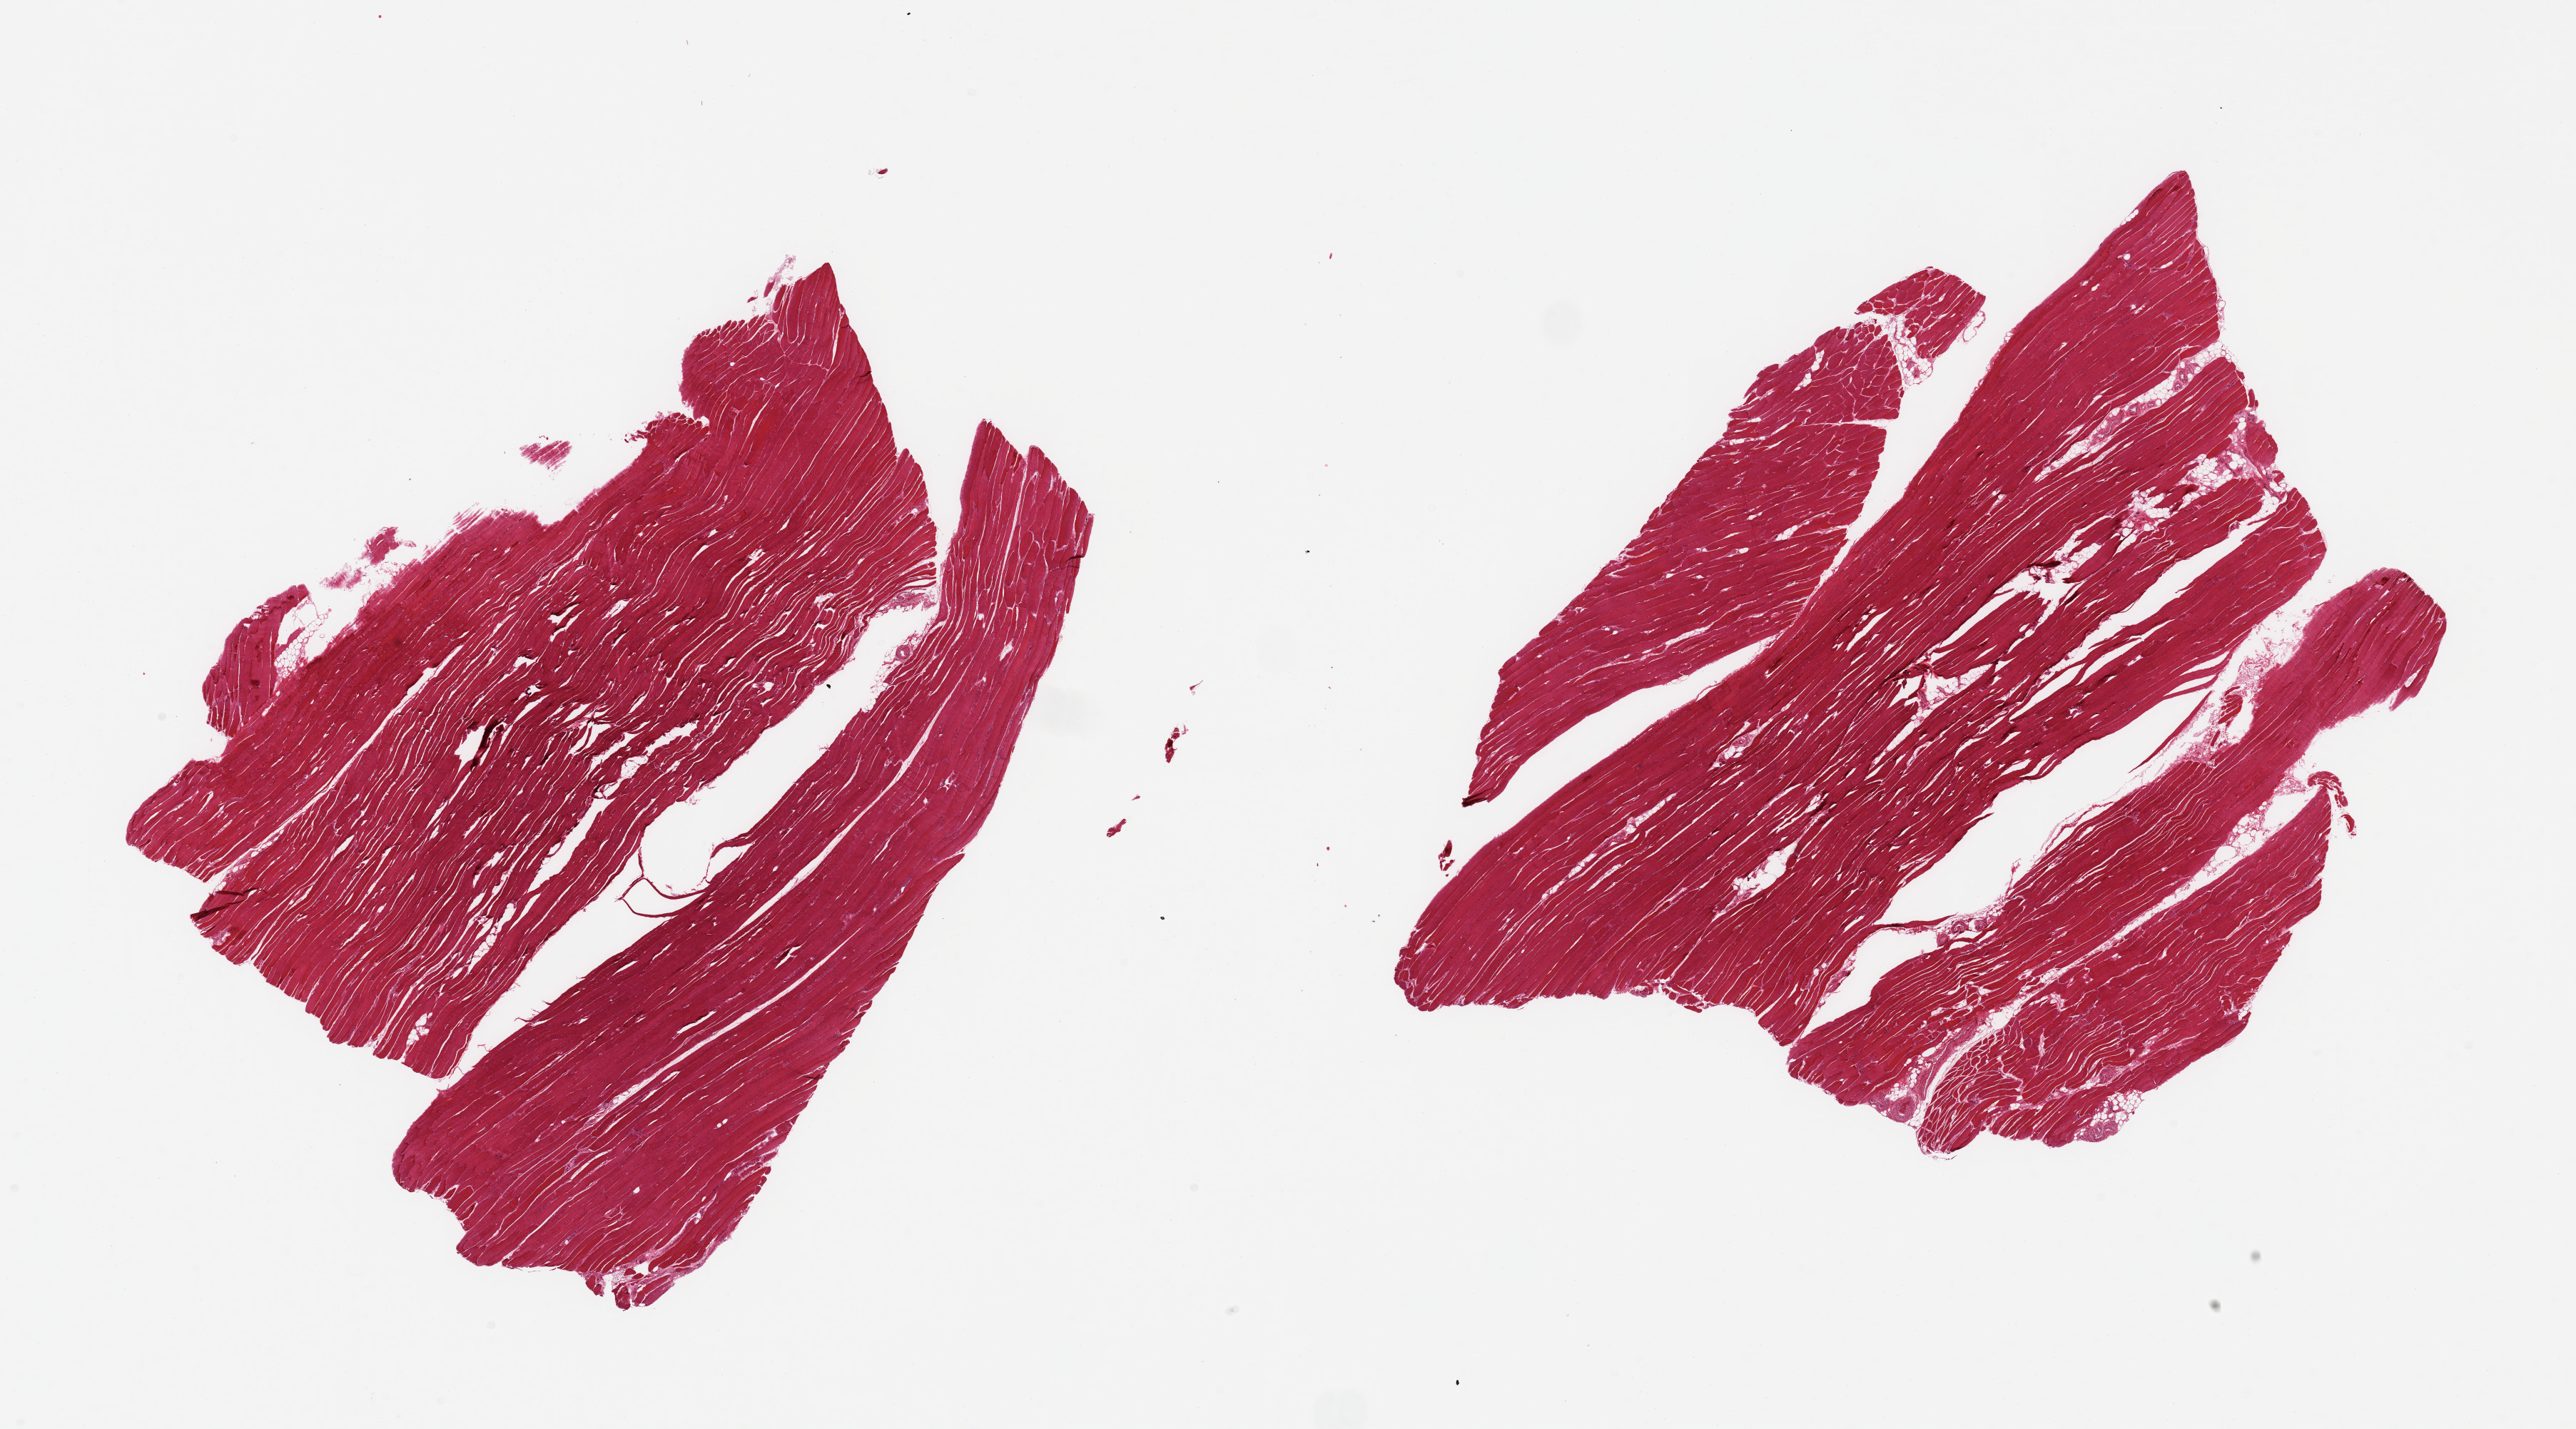
Digitized haematoxylin and eosin-stained section, shown as a low-resolution overview of the whole scanned area (about 28.5 x 15.8 mm), PAXgene-fixed, paraffin-embedded tissue, section of skeletal muscle (target tissue), donor tissue sample. Donor: male.
* review note (as recorded): 2 pieces; fragmented sections, small component of internal fat/vessels